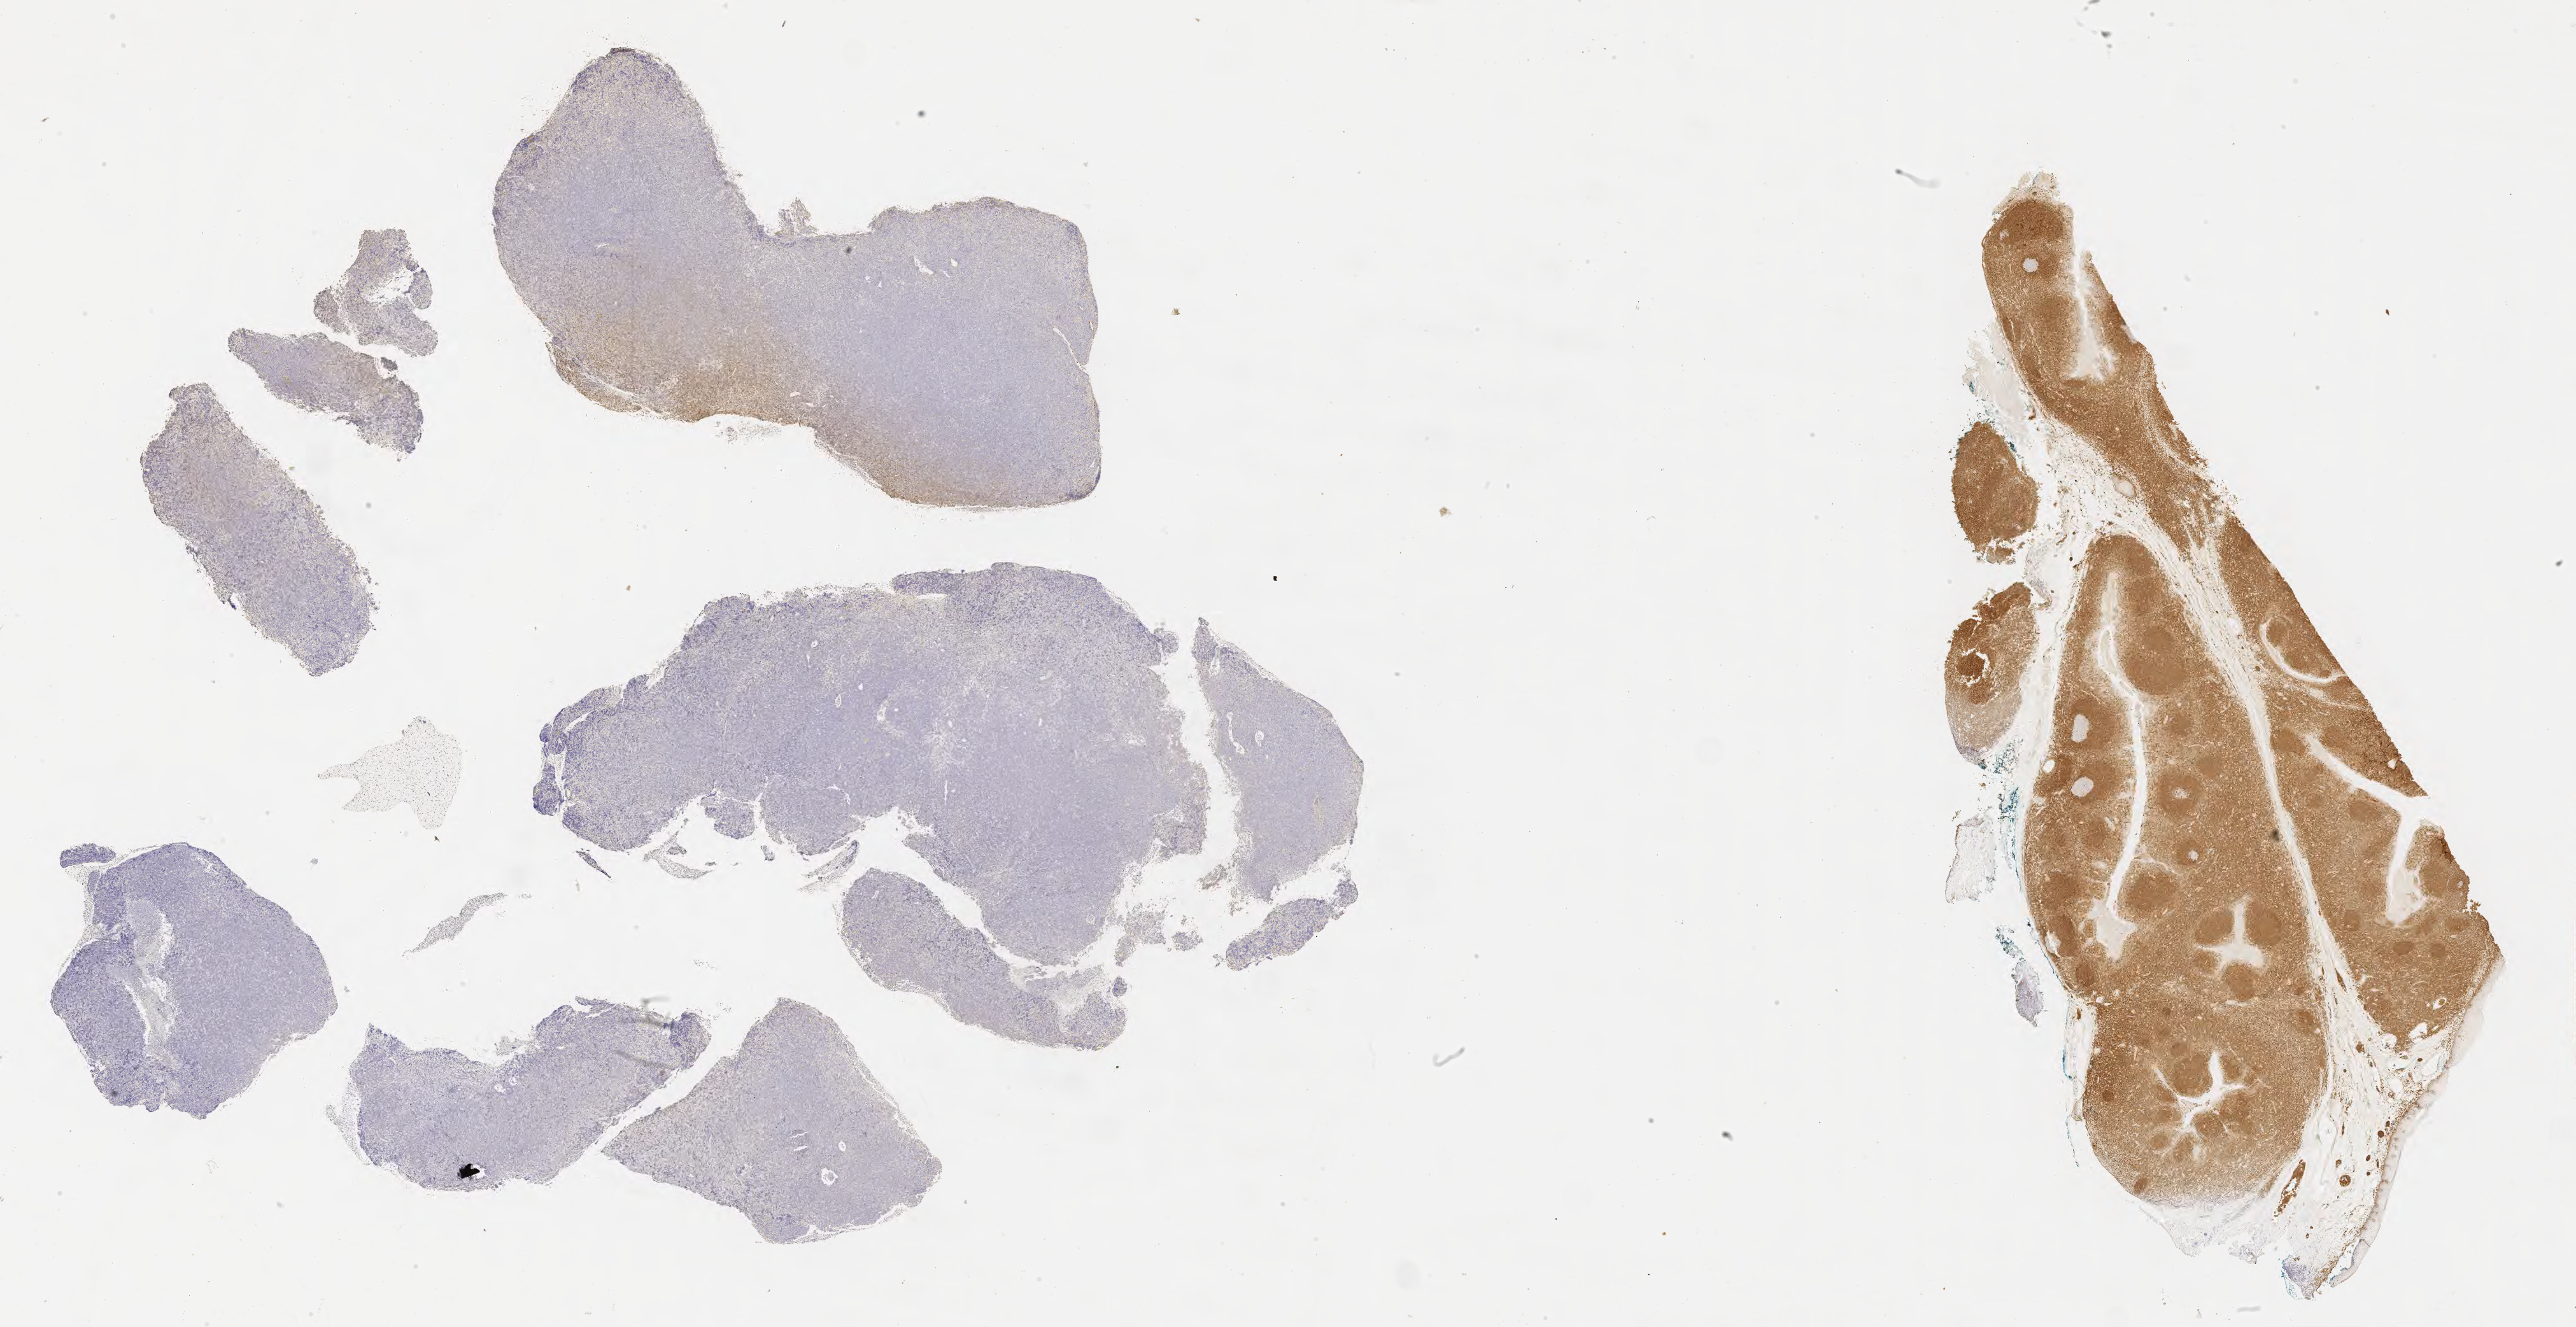
Whole-slide image, immunohistochemical stain for BCL2, whole scanned area (about 32.7 x 16.9 mm) shown as a low-resolution overview. Specimen: tumor tissue. Anatomic site: soft tissue. Female, age 9 years at initial diagnosis.
Diagnosis: Burkitt lymphoma, NOS.